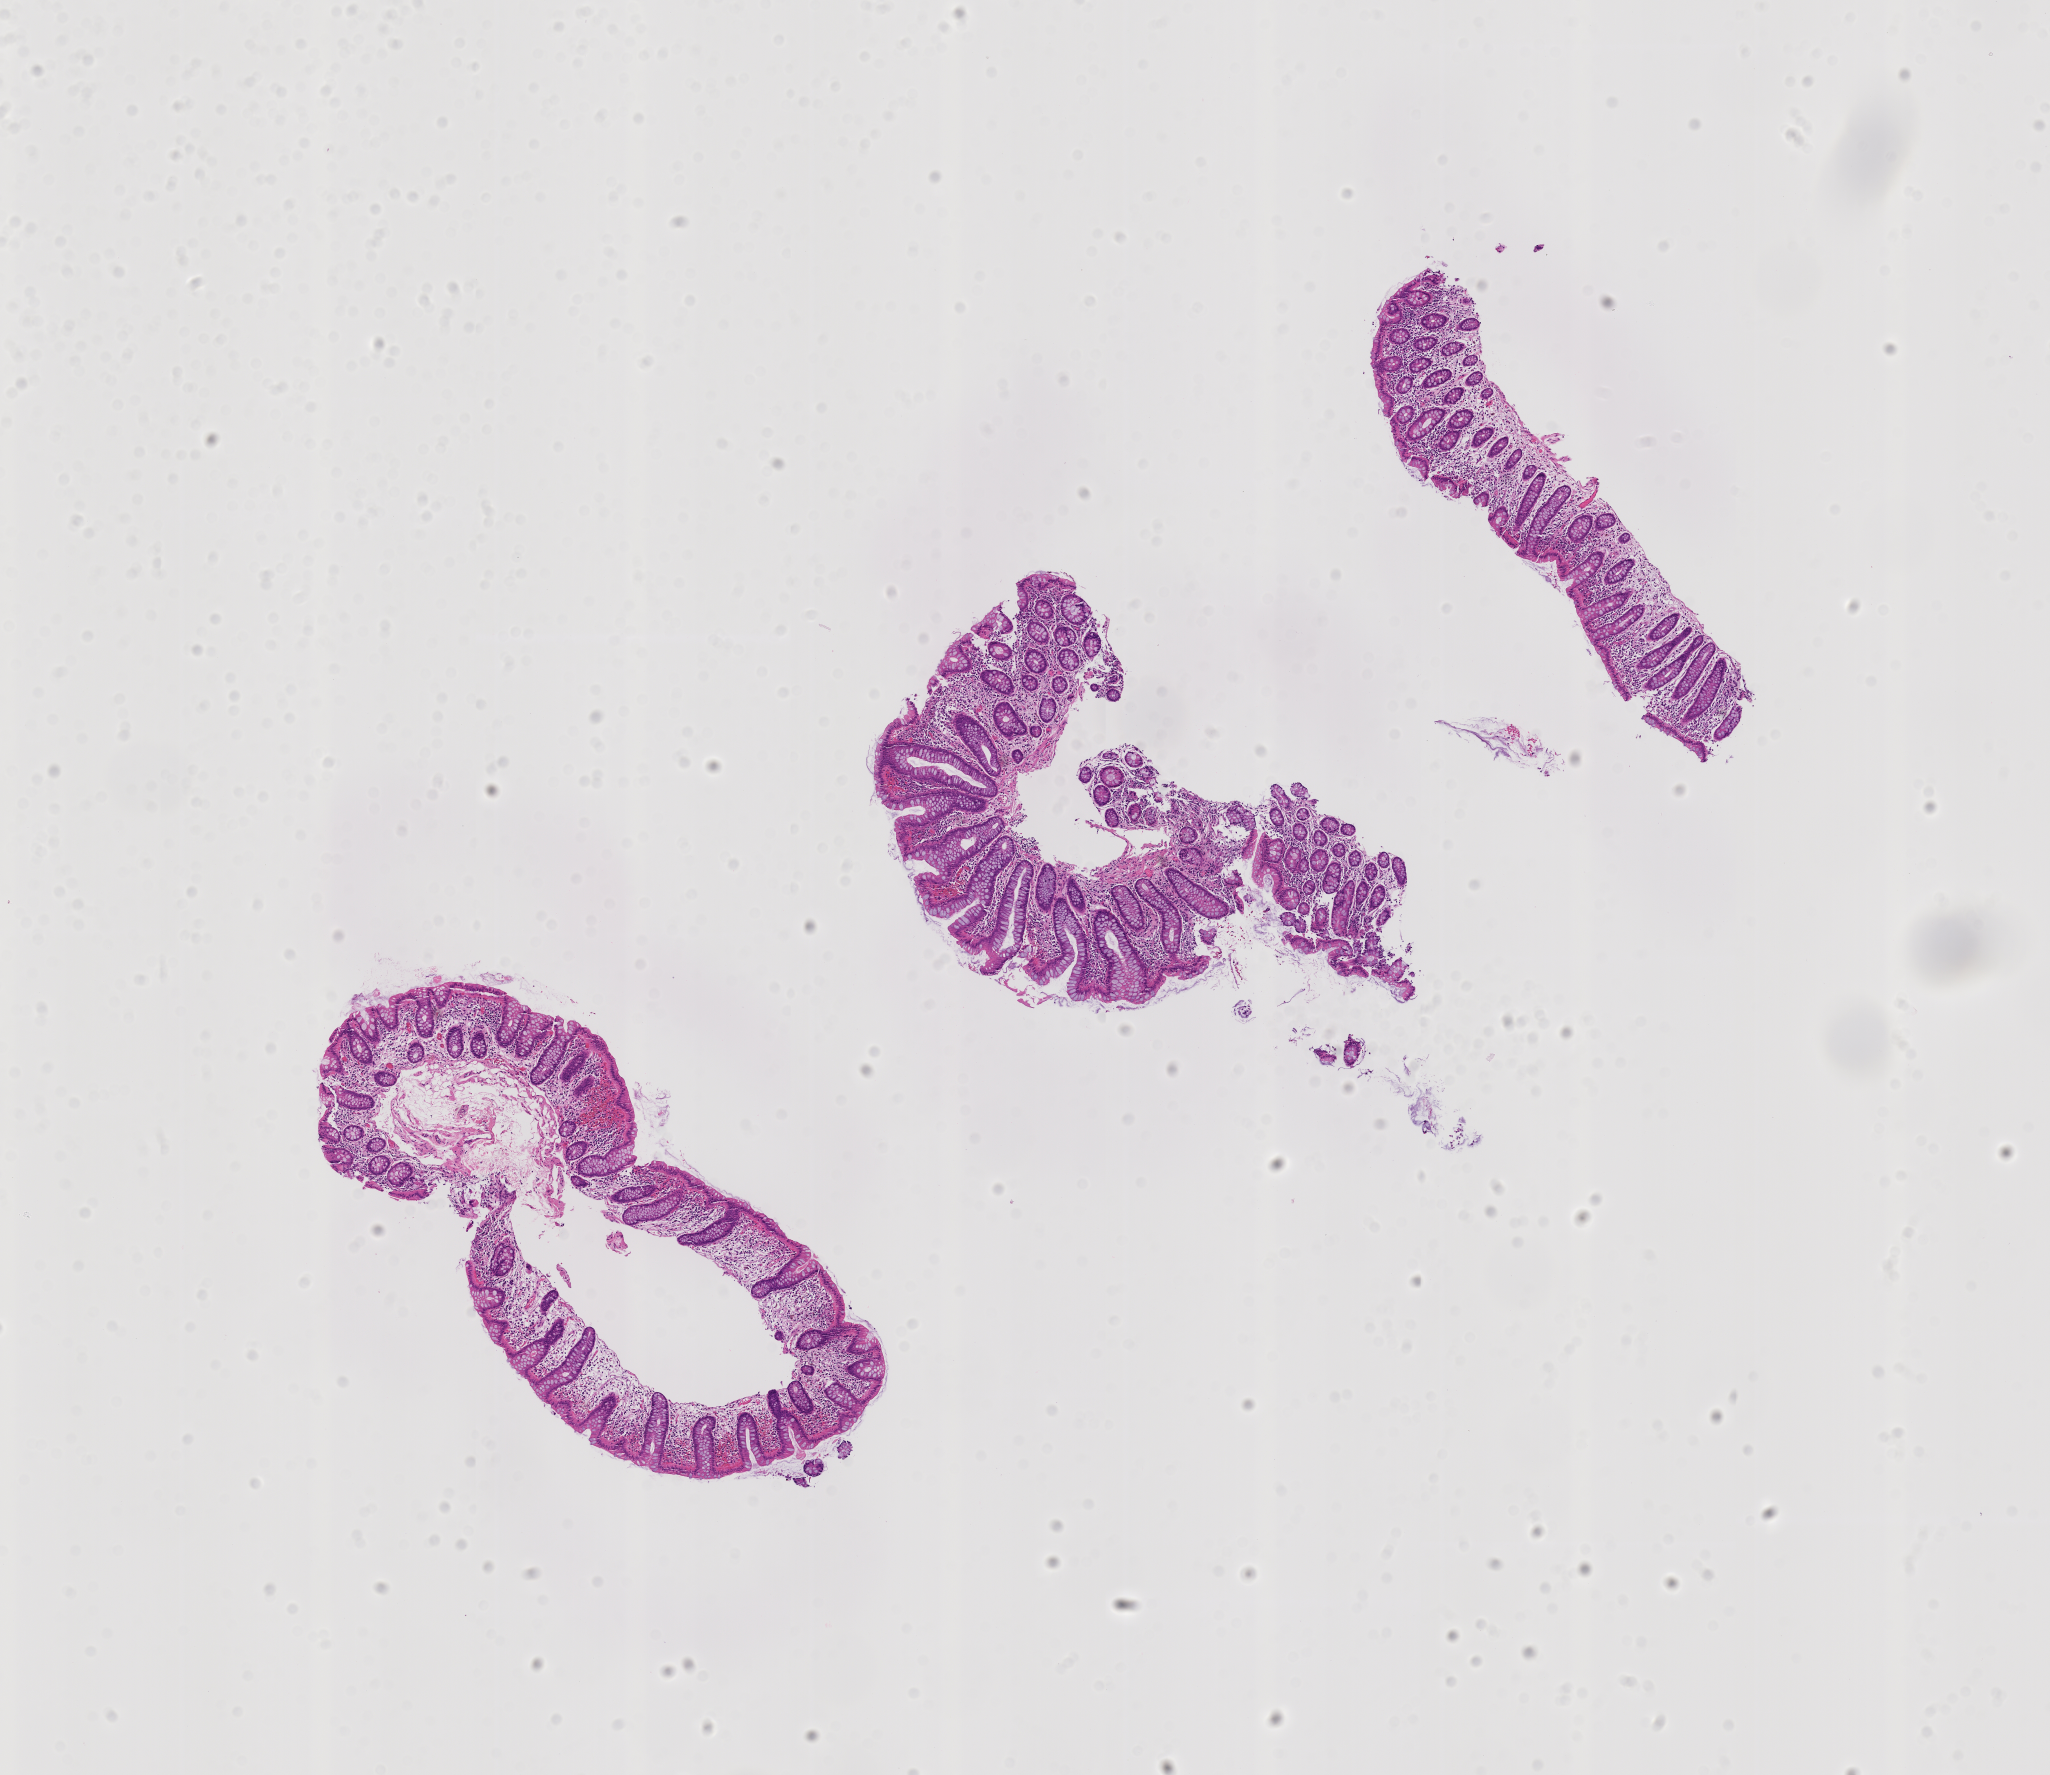
Whole-slide image, haematoxylin and eosin stain: colon biopsy — low-resolution overview of the scanned area, about 8.2 x 7.1 mm, formalin-fixed paraffin-embedded section, site: cecum. Patient: male.
Lesion category (as recorded): hyperplasia.